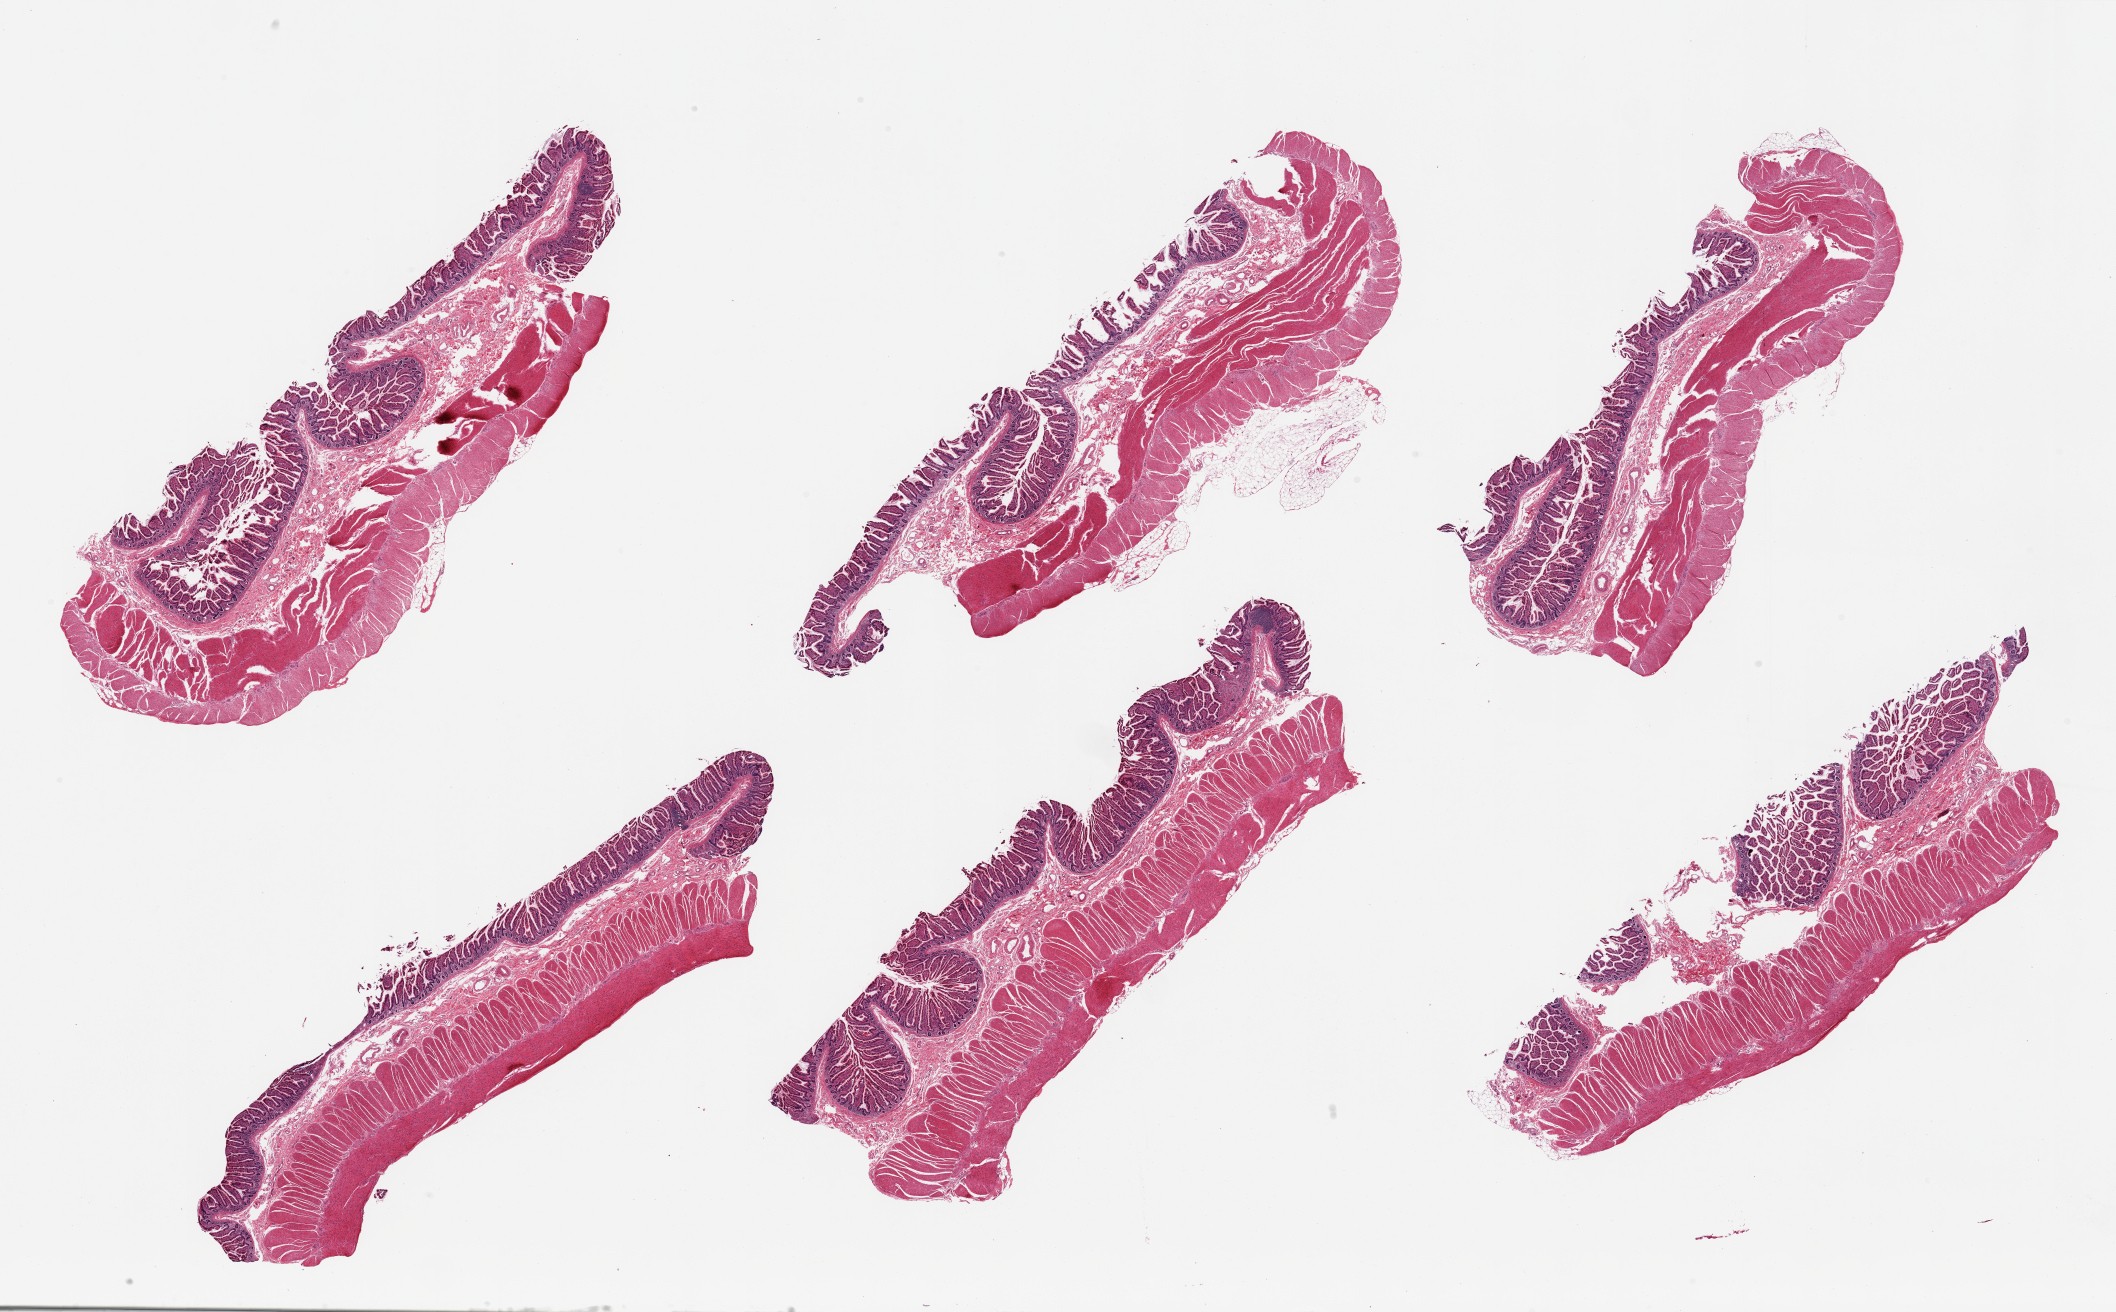
Whole-slide image, haematoxylin and eosin stain — low-resolution overview of the scanned area, about 33.5 x 20.8 mm, PAXgene-fixed, paraffin-embedded tissue, section of transverse colon (target tissue), tissue donor sample. Donor sex: female.
* reviewer comment on this tissue sample: 6 pieces, small intestine, not colon